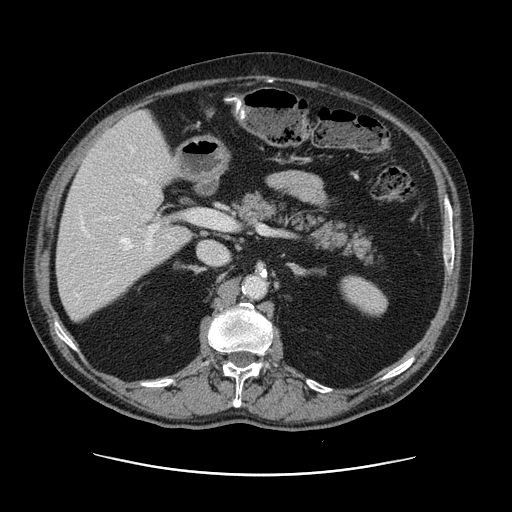
Contrast-enhanced abdominal CT, one axial slice. Position 69 of 141 along the scan axis. 120 kVp. Intravenous contrast given. Soft-tissue window (W 400 / L 40 HU). 2.5 mm slice thickness. 512 × 512 image matrix, field of view 395 × 395 mm. Male patient, age 72 years. From the clinical record (not read from this slice): diagnosis: colorectal cancer liver metastases, imaged before liver resection; multiple liver metastases: yes; largest metastasis: 5.4 cm.
Annotated regions visible in this slice (expert manual segmentation):
- hepatic veins: bounding box (x1, y1, x2, y2) in pixels: (120, 146, 147, 250)
- liver: (57, 113, 190, 320)
- planned liver remnant (the part of the liver to remain after resection): (57, 187, 190, 320)
- portal vein (with intrahepatic branches): (81, 199, 203, 251)